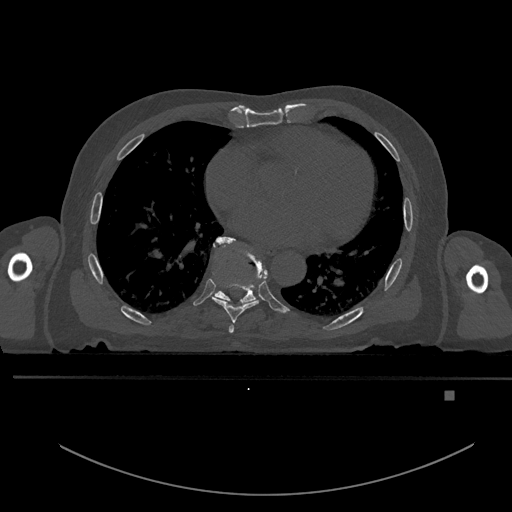
CT including the spine, one axial slice. Position 234 of 969 along the scan axis. Bone window (W 1800 / L 400 HU). 512 × 512 image matrix, field of view 456 × 456 mm. Patient: male, 82 years. Case-level facts recorded for this patient, not image findings: primary cancer: prostate; vertebrae with lytic lesions (as recorded): T11, T9, T8, T2.
Structures marked on this image (semi-automatic segmentation, software-assisted and operator-edited):
- T6 vertebra: bounding box [x1, y1, x2, y2] px = [228, 324, 234, 333]
- T7 vertebra: [212, 236, 268, 323]
- T8 vertebra: [212, 239, 262, 306]